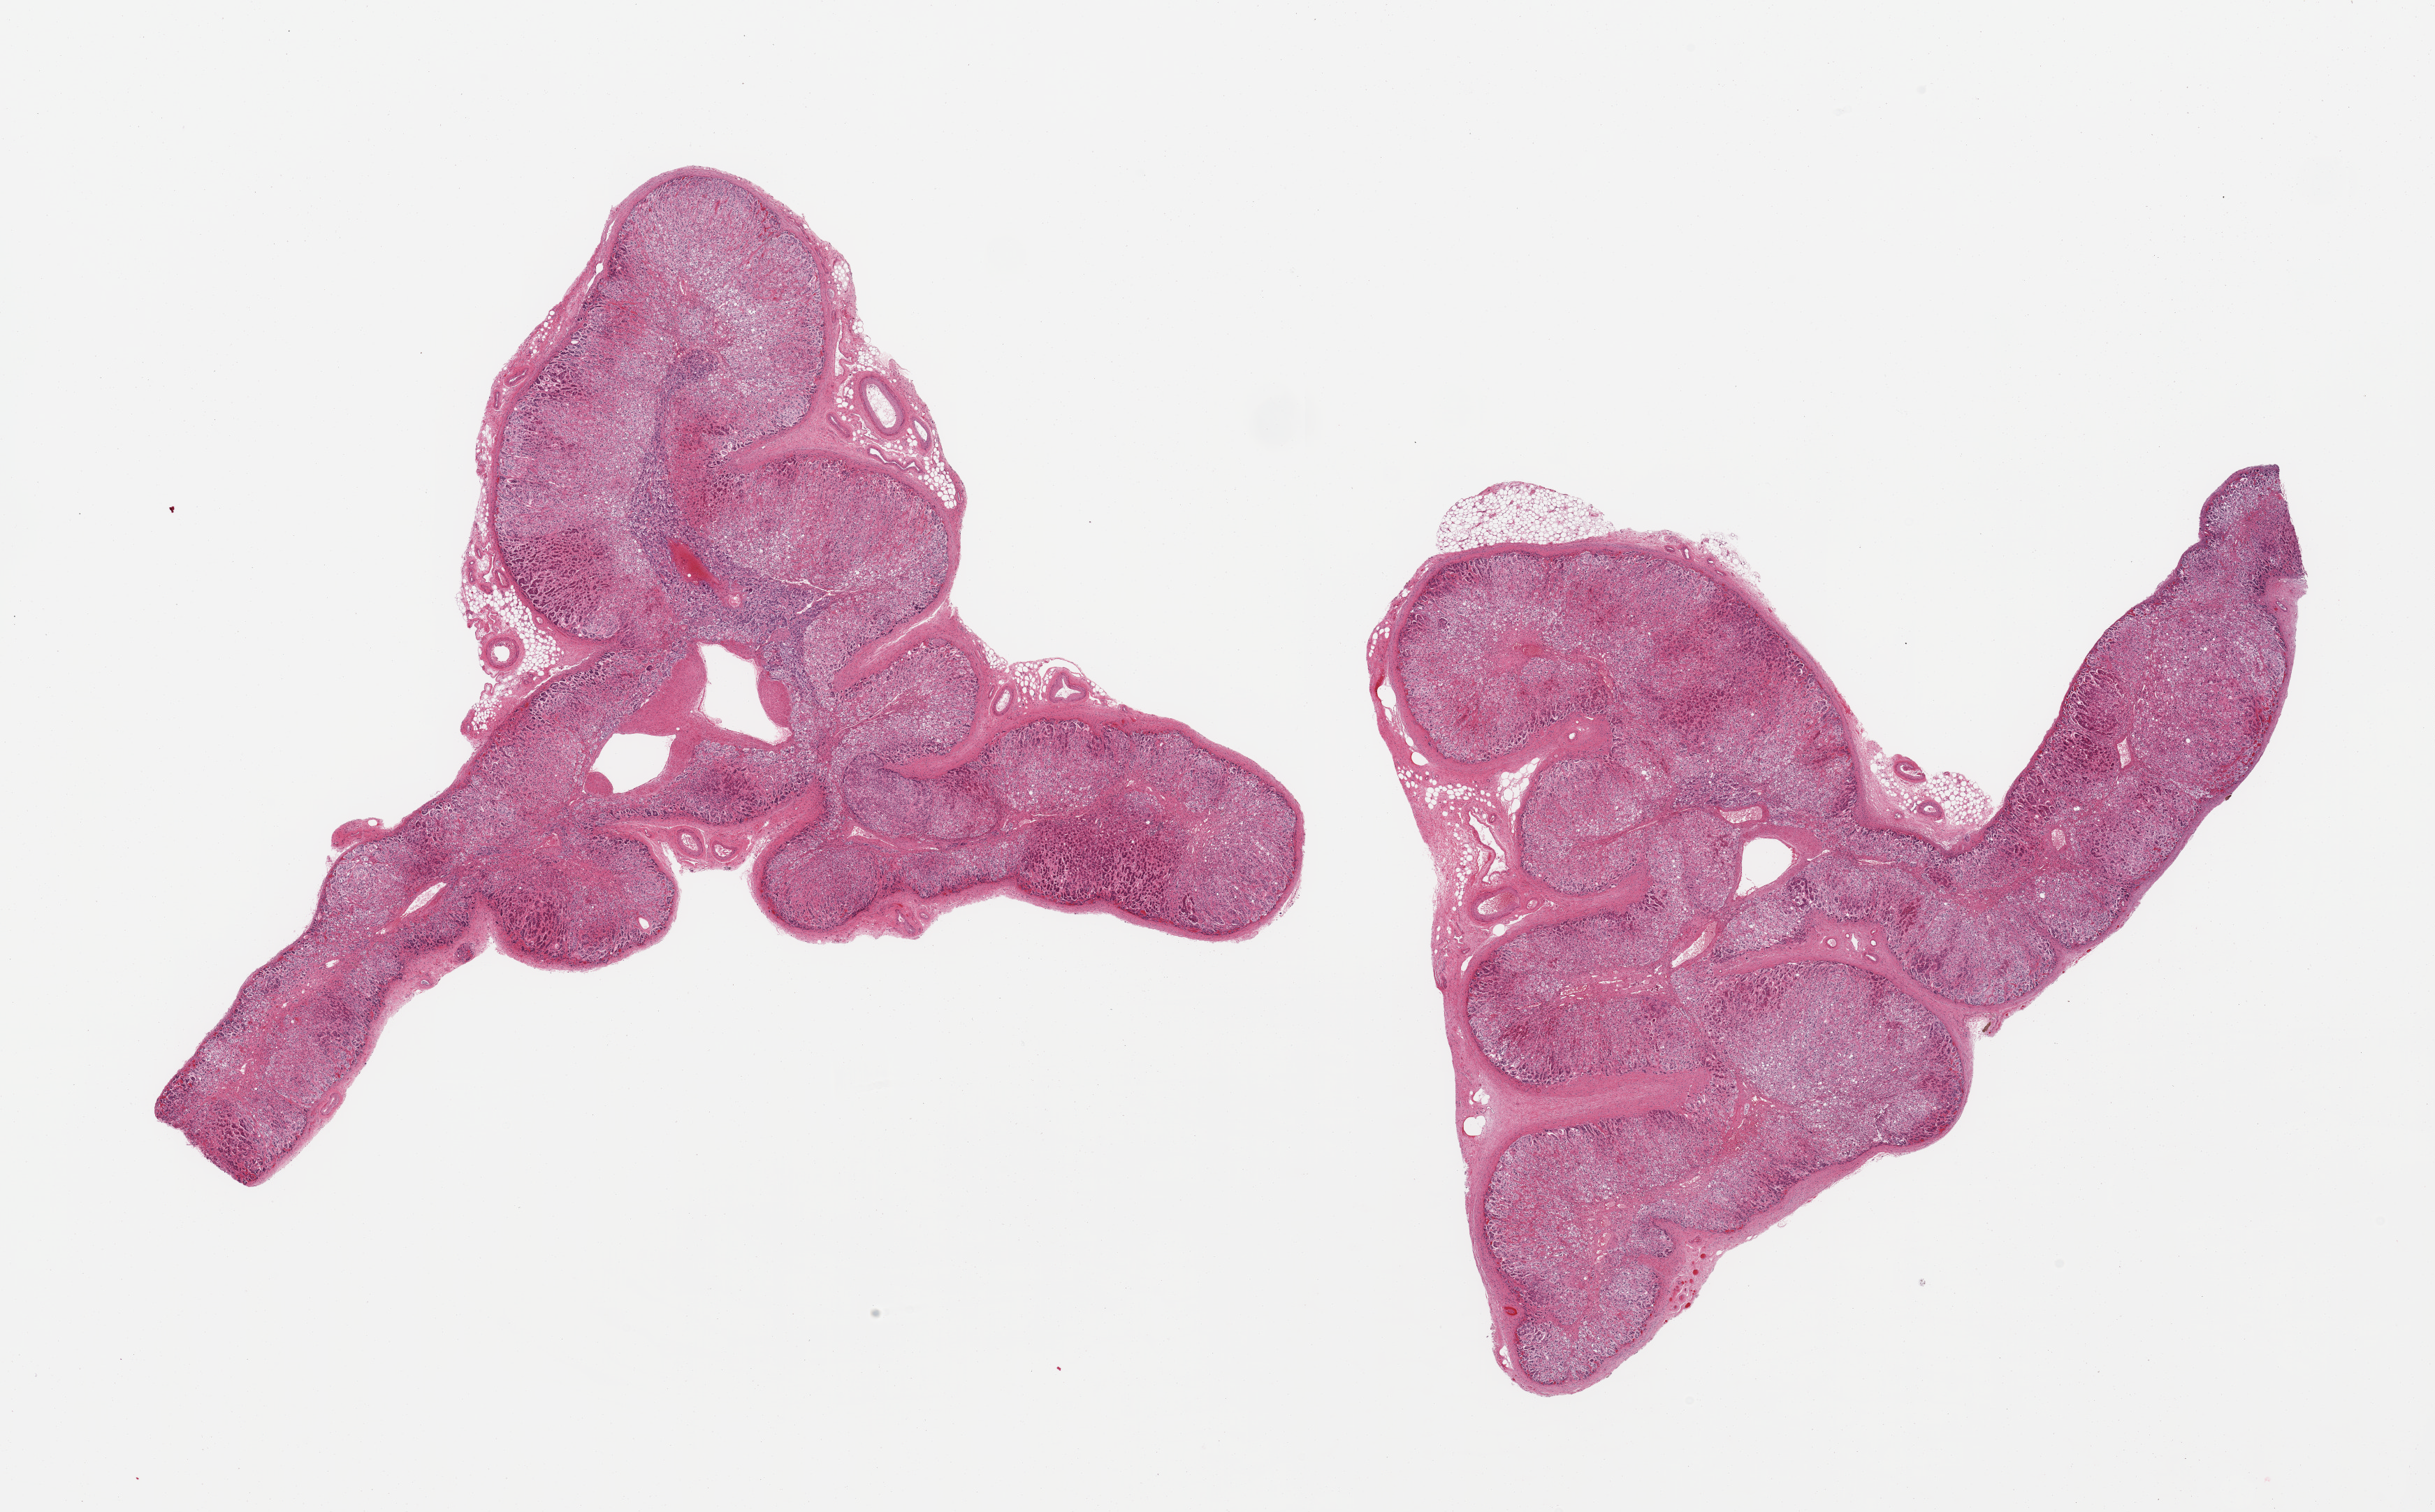
Whole-slide image, hematoxylin and eosin (H&E) stain, brightfield, shown as a low-resolution overview of the whole scanned area (about 27.6 x 17.1 mm), PAXgene-fixed paraffin-embedded (PFPE) section, target tissue: adrenal gland, donor tissue sample. Male donor.
* reviewer comment on this tissue sample: 2 pieces; moderate to severe focal autolysis of adrenal cortex, medulla; rim of adherent fat